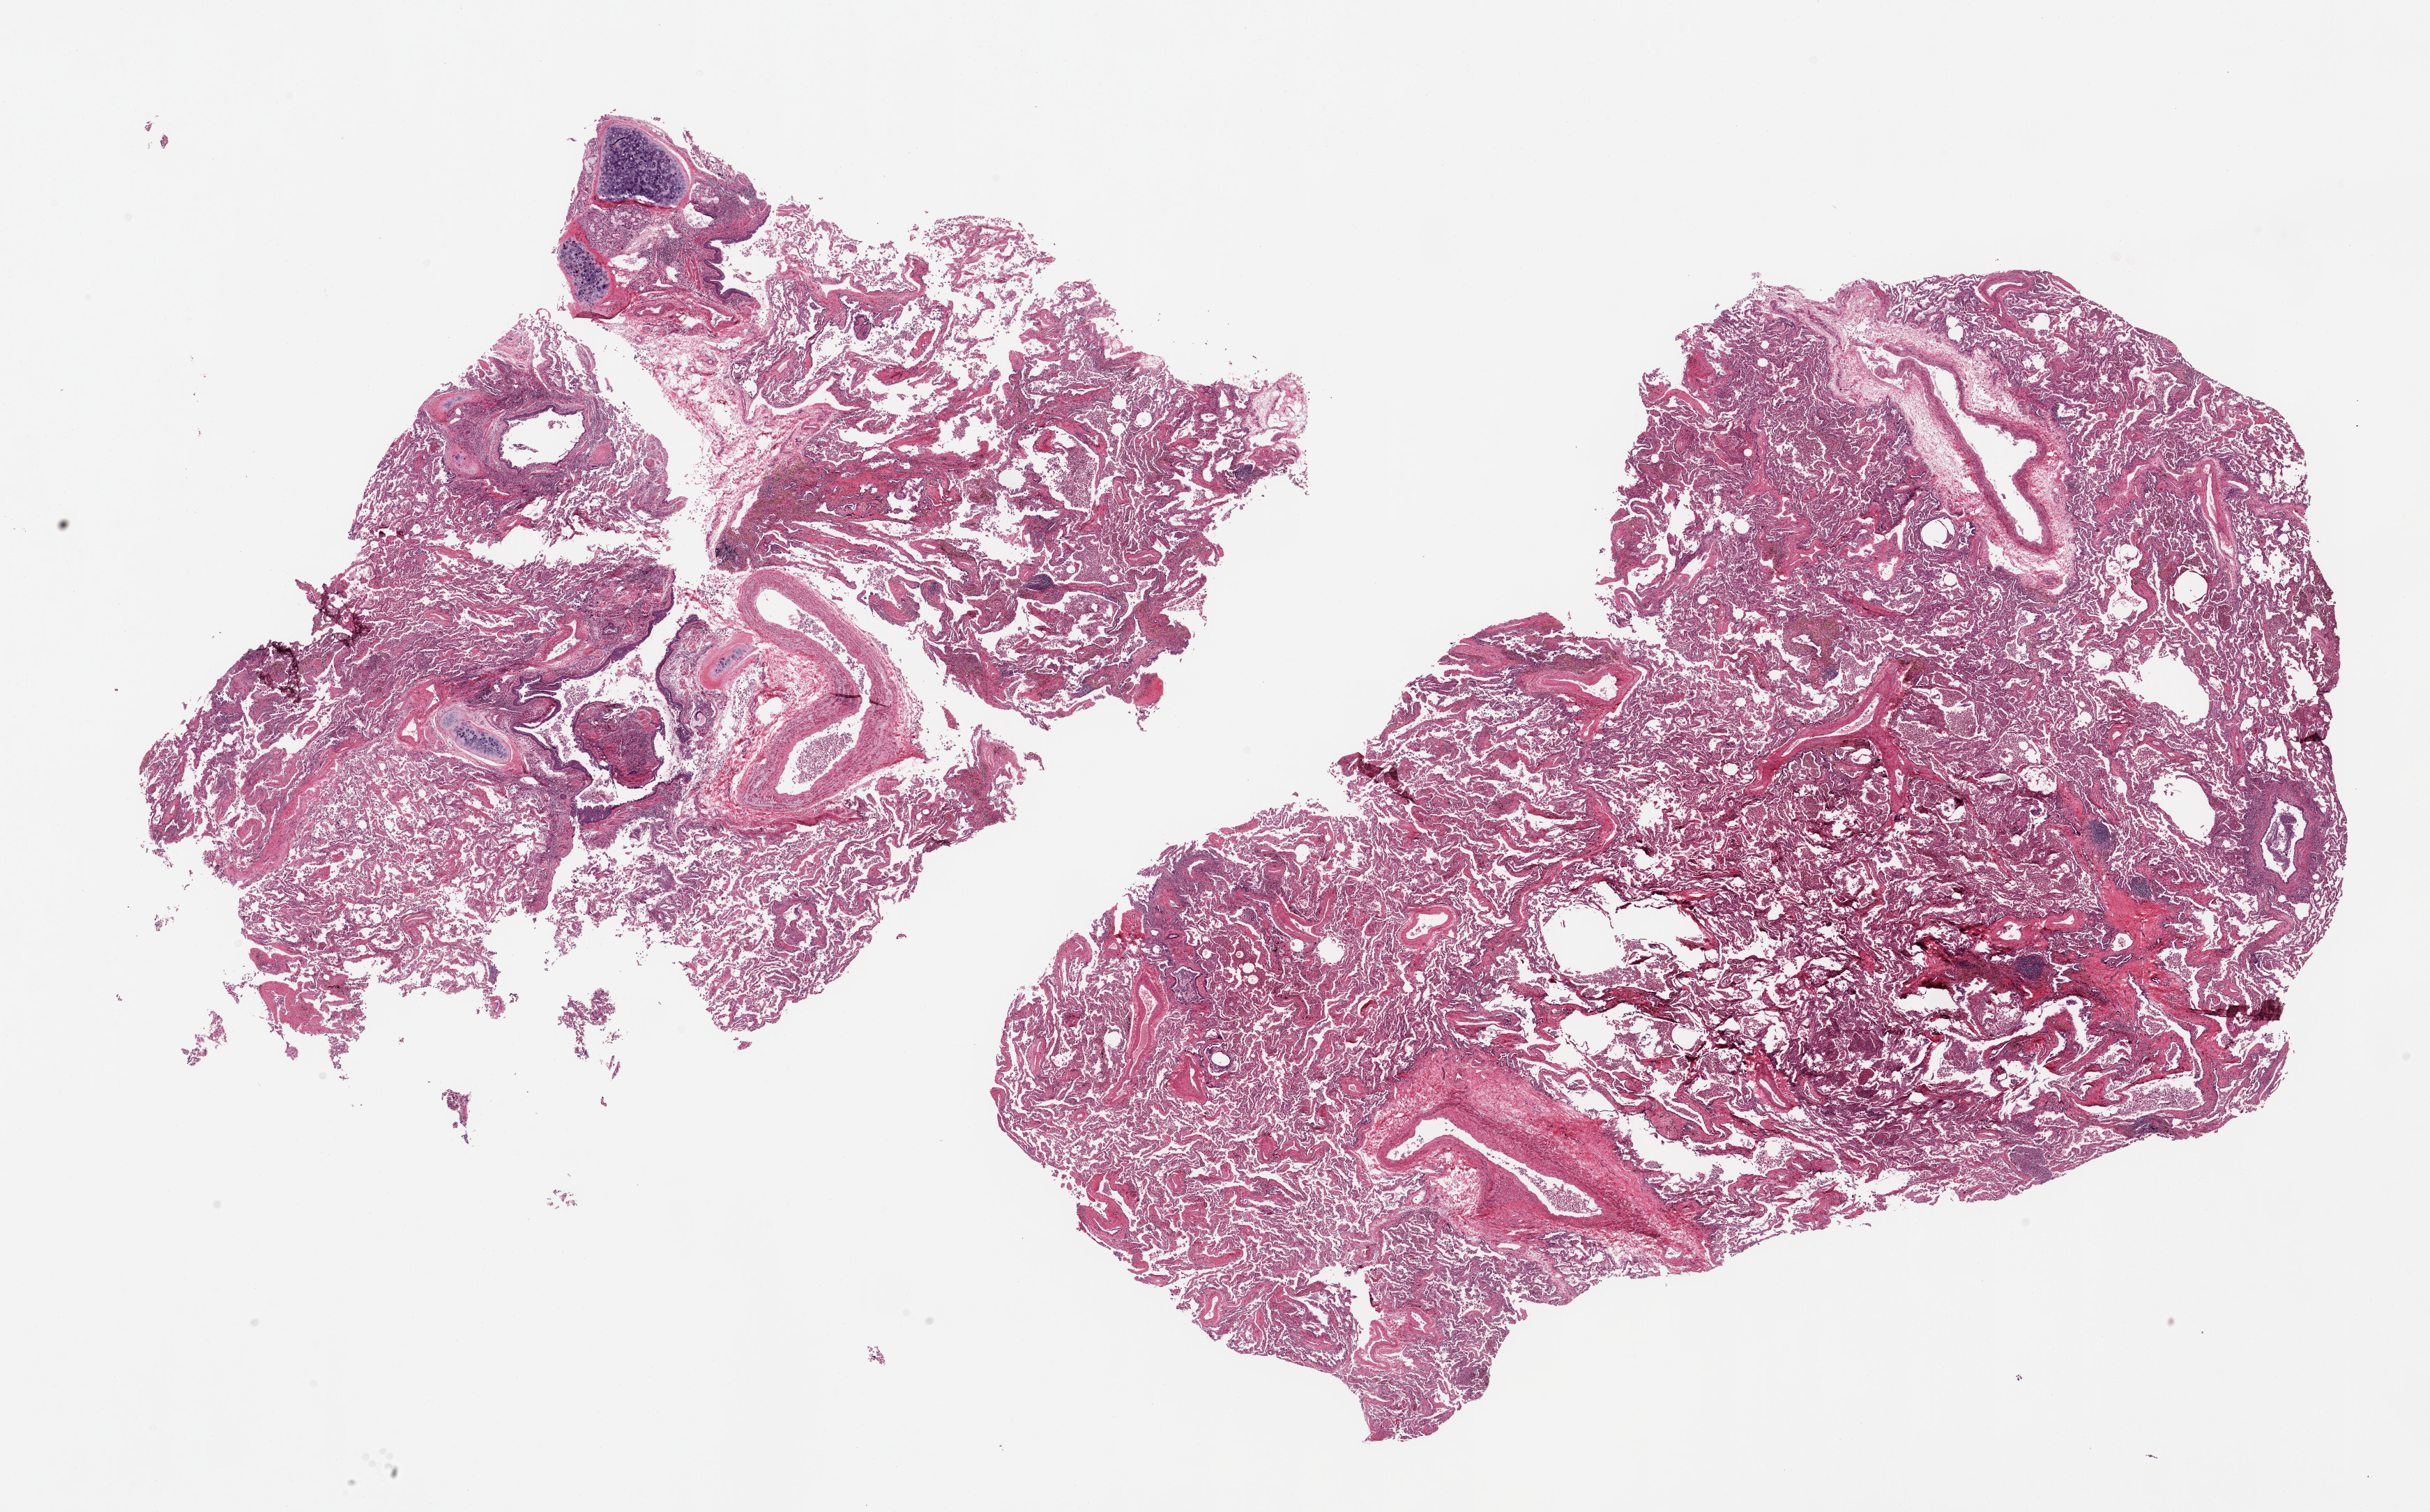
Whole-slide image, haematoxylin and eosin stain — whole scanned area (about 27.6 x 17.2 mm) shown as a low-resolution overview; PAXgene-fixed paraffin-embedded (PFPE) section; section of lung (target tissue); donor tissue sample. Female donor.
* review note (as recorded): 2 pieces, pronounced chronic congestion, mild active pneumonitis/bronchitis; bronchial hyaline cartilage present